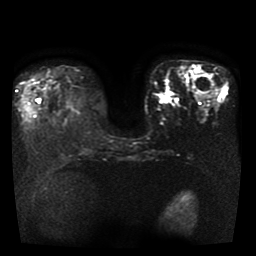
Breast MRI, one axial slice. Slice 14 of 41 in the series (ordered by position). Diffusion-weighted series; image 2 of 4 stored at this slice position (different b-values; order by instance number). 1.5 T. 5 mm slice thickness. 256 × 256 image matrix, field of view 330 × 330 mm. Female patient.
Annotated regions visible in this slice (expert manual segmentation):
- tumour on diffusion-weighted imaging: box from (x=161, y=92) to (x=174, y=102) px